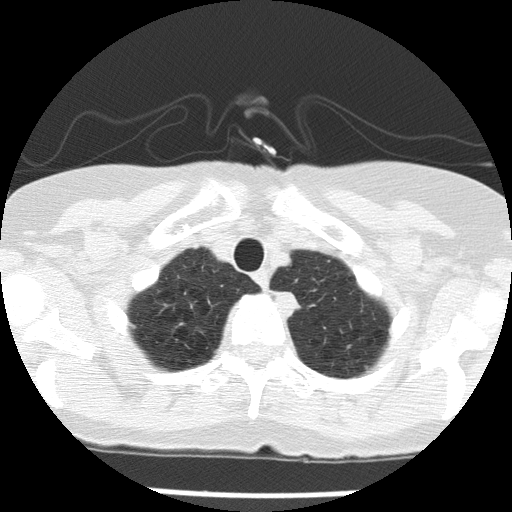
Axial slice from a low-dose chest CT screening exam, first (baseline) screen, lung window (W 1500 / L -600 HU), slice 16 of 143 in the series, 512 × 512 image matrix. Female participant, aged 74 years at enrolment. Former smoker at enrolment.
Expert-annotated lung lesion, box from (x=268, y=288) to (x=306, y=319) px. The screening reader recorded 2 non-calcified nodules or masses ≥4 mm on this exam; which of them this box marks is not recorded. Lung cancer was diagnosed 81 days after this screen: adenocarcinoma, NOS, left upper lobe, poorly differentiated (G3), stage IA (AJCC 6th edition), 24 mm at pathology.